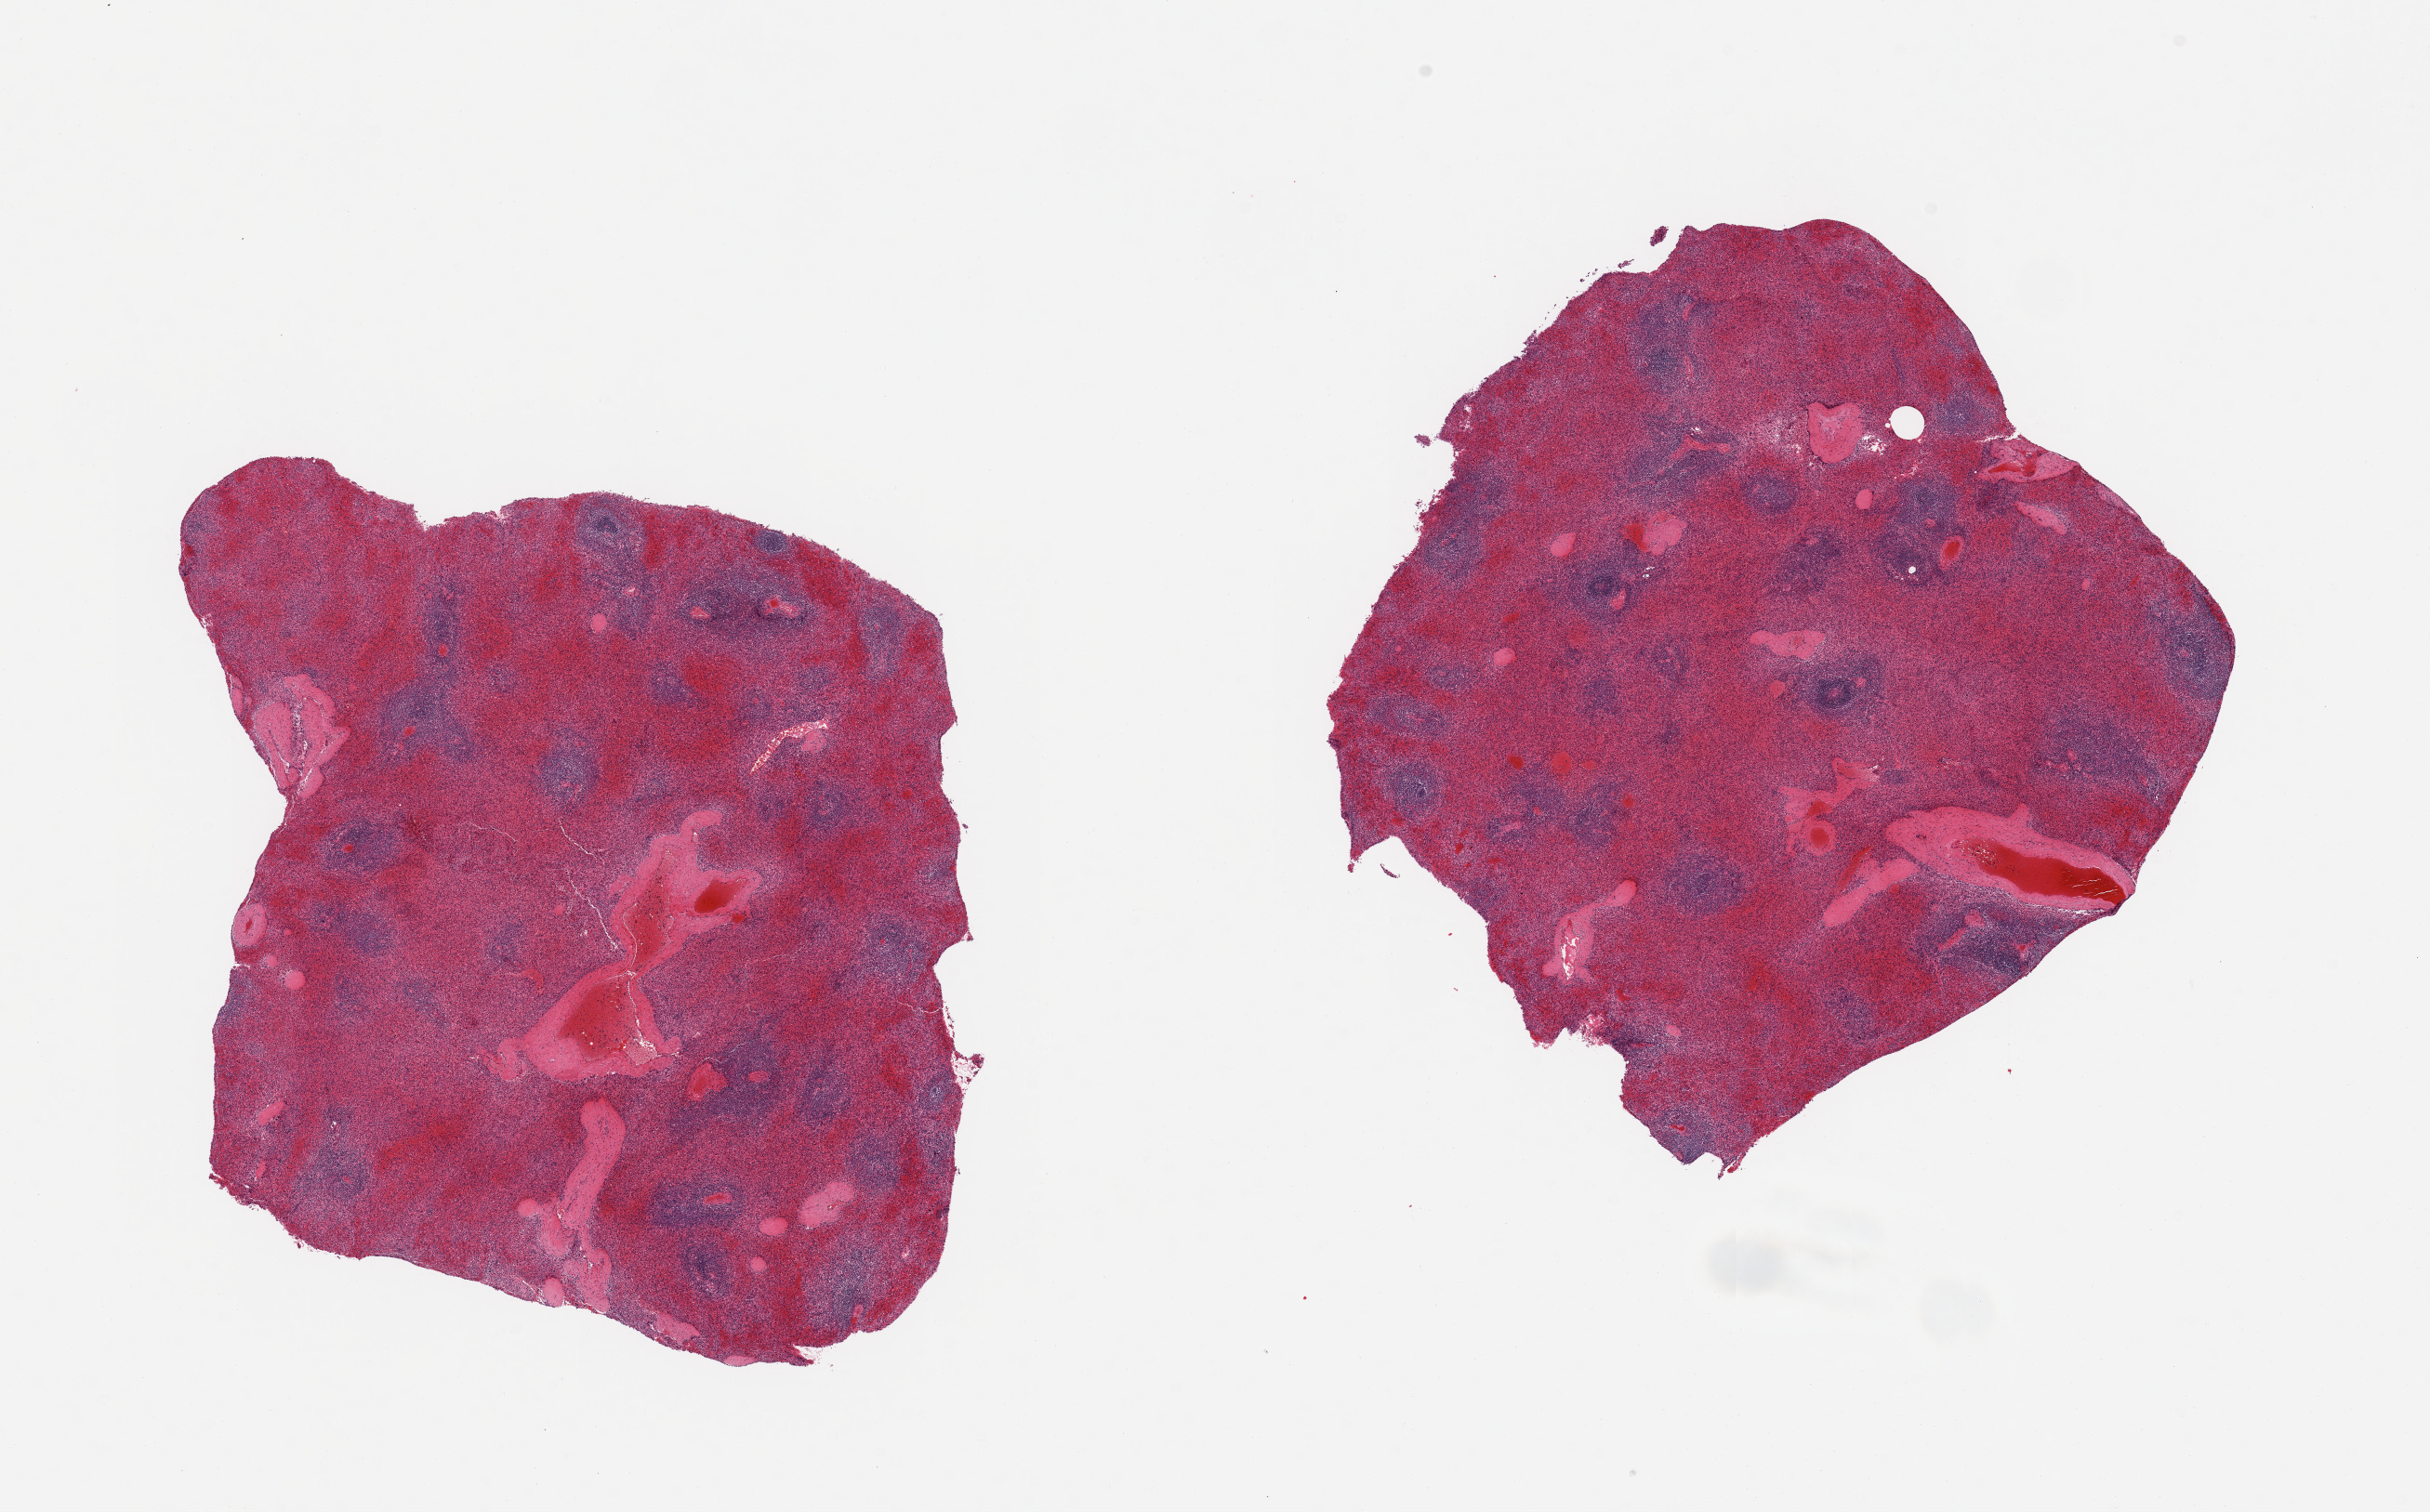
Digitized H&E-stained section, brightfield — low-resolution overview of the scanned area, about 20.7 x 12.9 mm; PAXgene-fixed paraffin-embedded (PFPE) section; target tissue: spleen; donor tissue sample. Donor sex: male.
Review note (as recorded): 2 pieces; moderate vascular & red pulp congestion; well defined lymphoid tissue.